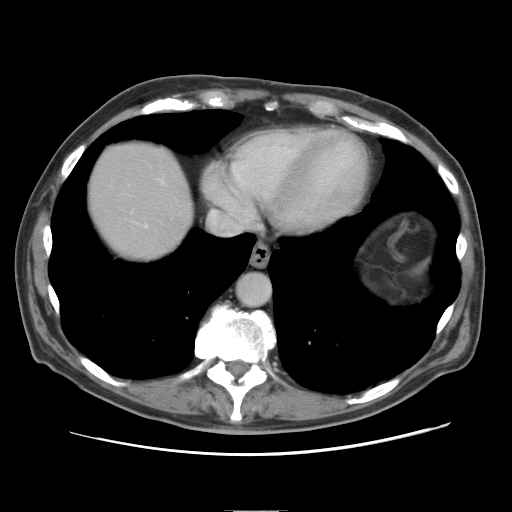
Contrast-enhanced abdominal CT, one axial slice. 120 kVp. Intravenous contrast given. Soft-tissue window (W 400 / L 40 HU). 5 mm slice thickness. 512 × 512 image matrix, field of view 375 × 375 mm. Male patient, age 69 years. Case-level facts recorded for this patient, not image findings: diagnosis: colorectal cancer liver metastases, imaged before liver resection; multiple liver metastases: no; largest metastasis: 8.5 cm; disease in both lobes: no.
Annotated regions visible in this slice (outlined manually by an expert reader):
- liver: bounding box <88,143,192,258> (left, top, right, bottom; pixels)
- planned liver remnant (the part of the liver to remain after resection): <89,143,192,258>